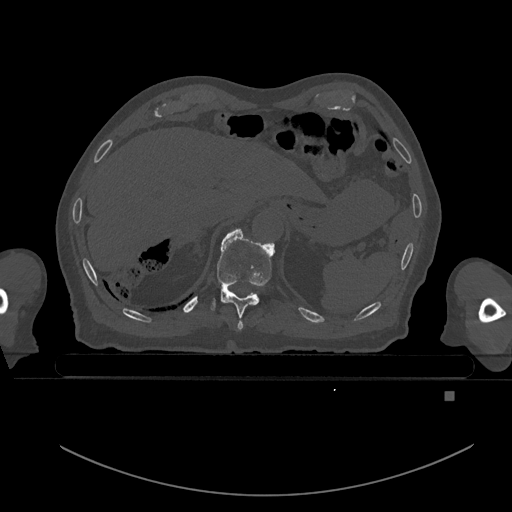
CT including the spine, one axial slice. Bone window (W 1800 / L 400 HU). 0.5 mm slice thickness. 512 × 512 image matrix, field of view 456 × 456 mm. Patient: male, 82 years. From the clinical record (not read from this slice): primary cancer: prostate; vertebrae with lytic lesions (as recorded): T11, T9, T8, T2.
Structures marked on this image (semi-automatically segmented with operator editing):
- T10 vertebra: box from (x=210, y=229) to (x=275, y=330) px